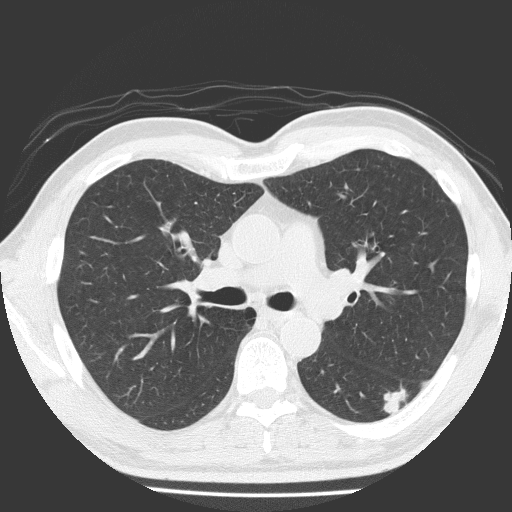
Chest CT (low-dose screening protocol), one axial image, first (baseline) screen, lung window (W 1500 / L -600 HU), 2 mm slice thickness, 120 kVp, 512 × 512 image matrix, field of view 348 × 348 mm. Male, age 58 years at enrolment. Current smoker at enrolment.
Expert reader's lesion annotation, box from (x=373, y=374) to (x=424, y=422) px. The screening reader recorded 4 non-calcified nodules or masses ≥4 mm on this exam (left lower lobe, left lower lobe, right middle lobe, left upper lobe); which of them this box marks is not recorded. Official screen result: positive, change unspecified: nodule(s) >= 4 mm or enlarging nodule(s), mass(es), or other non-specific abnormalities suspicious for lung cancer.